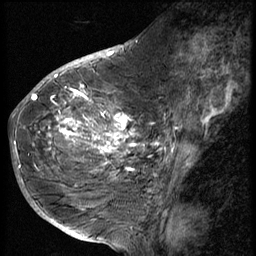
Breast MRI (dynamic contrast-enhanced), one sagittal slice; 3 images stored at this slice position (order not interpretable as contrast timing); 1.5 T; TE 4.2 ms, TR 9 ms; 2.5 mm slice thickness; 256 × 256 image matrix. Patient: female, 49 years. From the clinical record (not read from this slice): setting: breast cancer imaged before/during neoadjuvant chemotherapy; receptor status: HER2-positive.
Structures marked on this image (semi-automatically segmented with operator editing):
- analysis volume of interest (the breast-tissue region the enhancement analysis was run in; not a lesion): bounding box <37,85,136,207> (left, top, right, bottom; pixels)
- tumour enhancement mask (voxels above the 140 % enhancement threshold inside the analysis volume of interest): <41,85,134,178>